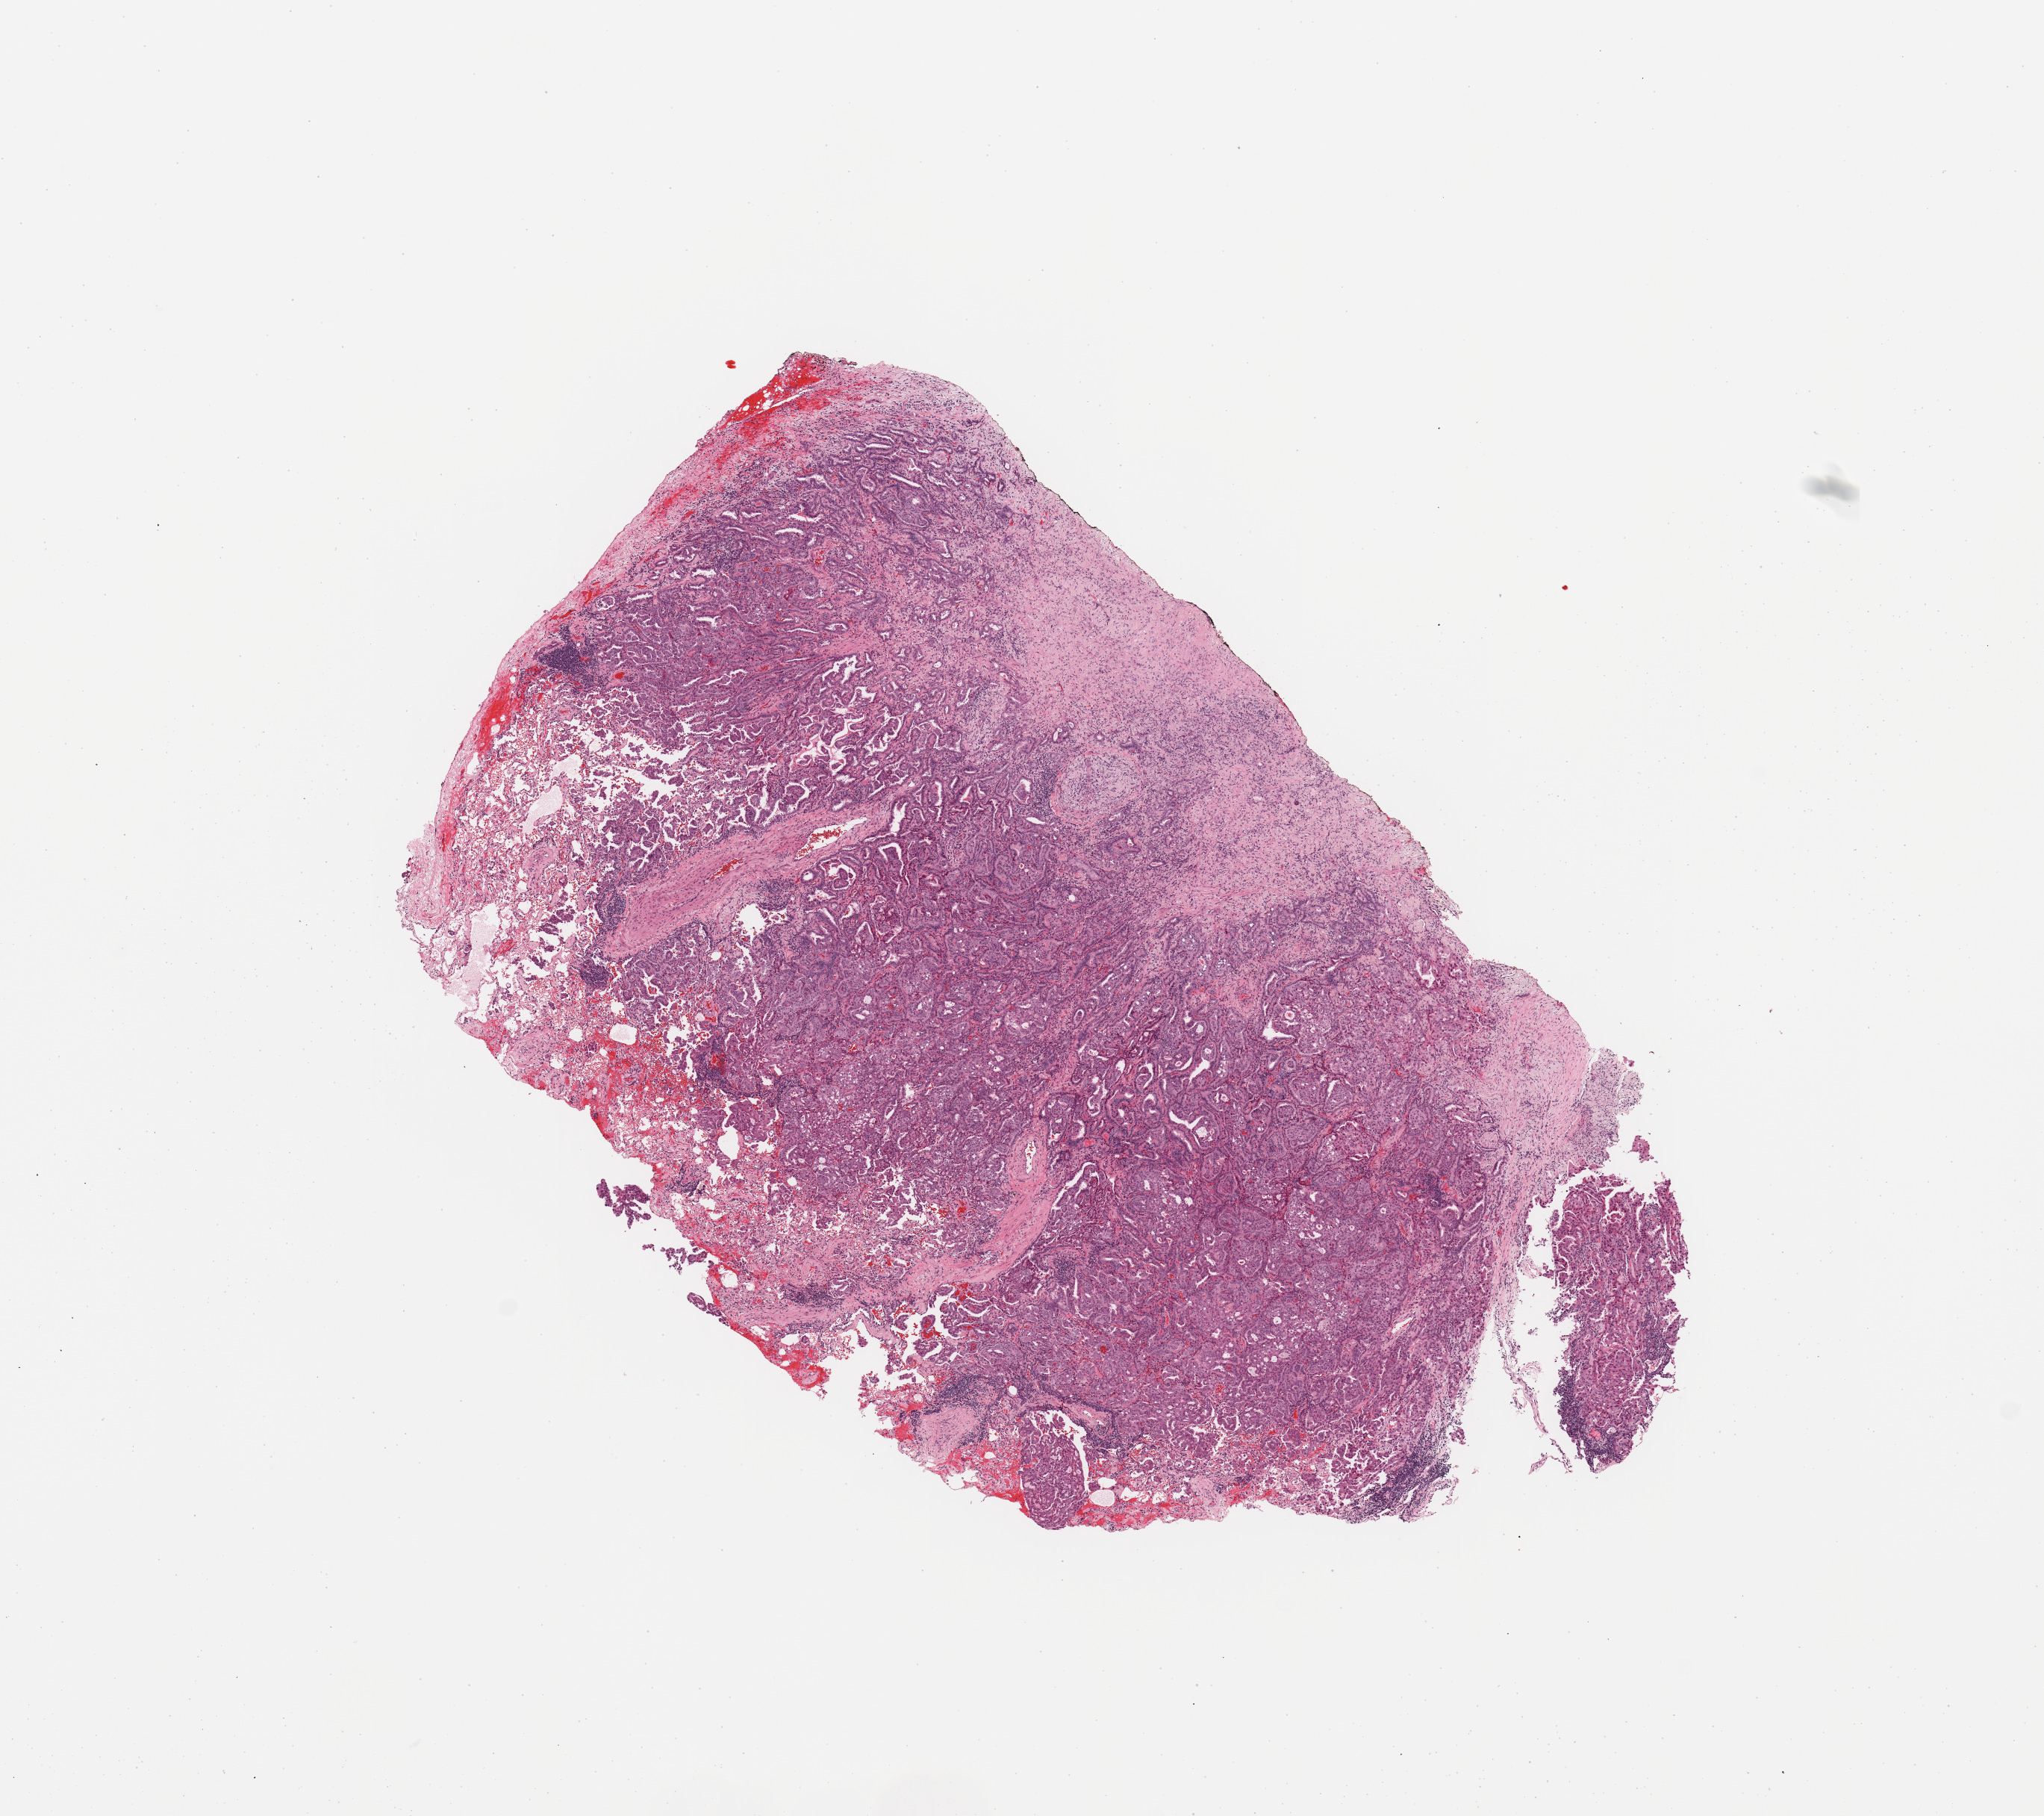
Whole-slide histology image, Hematoxylin and eosin (H&E) stained, shown as a low-resolution overview of the whole scanned area (about 10.8 x 9.6 mm). Tumour tissue sample, sampled site: lung. 73-year-old female patient. Histologic grade: G2 (moderately differentiated). Pathologist review of this section (percent, as recorded): tumour nuclei 75%, necrosis 2%.
Primary tumour site (as recorded): left upper lobe. Histologic diagnosis: Adenocarcinoma, NOS. AJCC pathologic stage: IA.